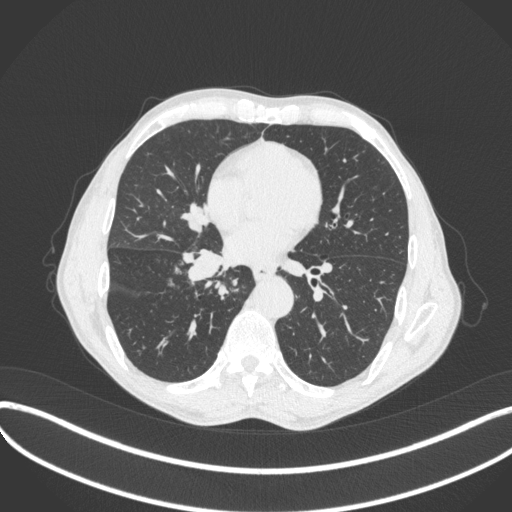
Chest CT, one axial slice. Slice 195 of 481 in the series (ordered by position). Reconstruction kernel B31f. Lung window (W 1500 / L -600 HU). 512 × 512 image matrix. Male patient, age 65 years. Case-level facts recorded for this patient, not image findings: clinical TNM (as recorded): T2a N0 M0; histopathological grade: G2.
Annotated regions visible in this slice (bounding box drawn by a radiologist):
- lung tumour (recorded histology: squamous cell carcinoma): box from (x=180, y=246) to (x=233, y=282) px